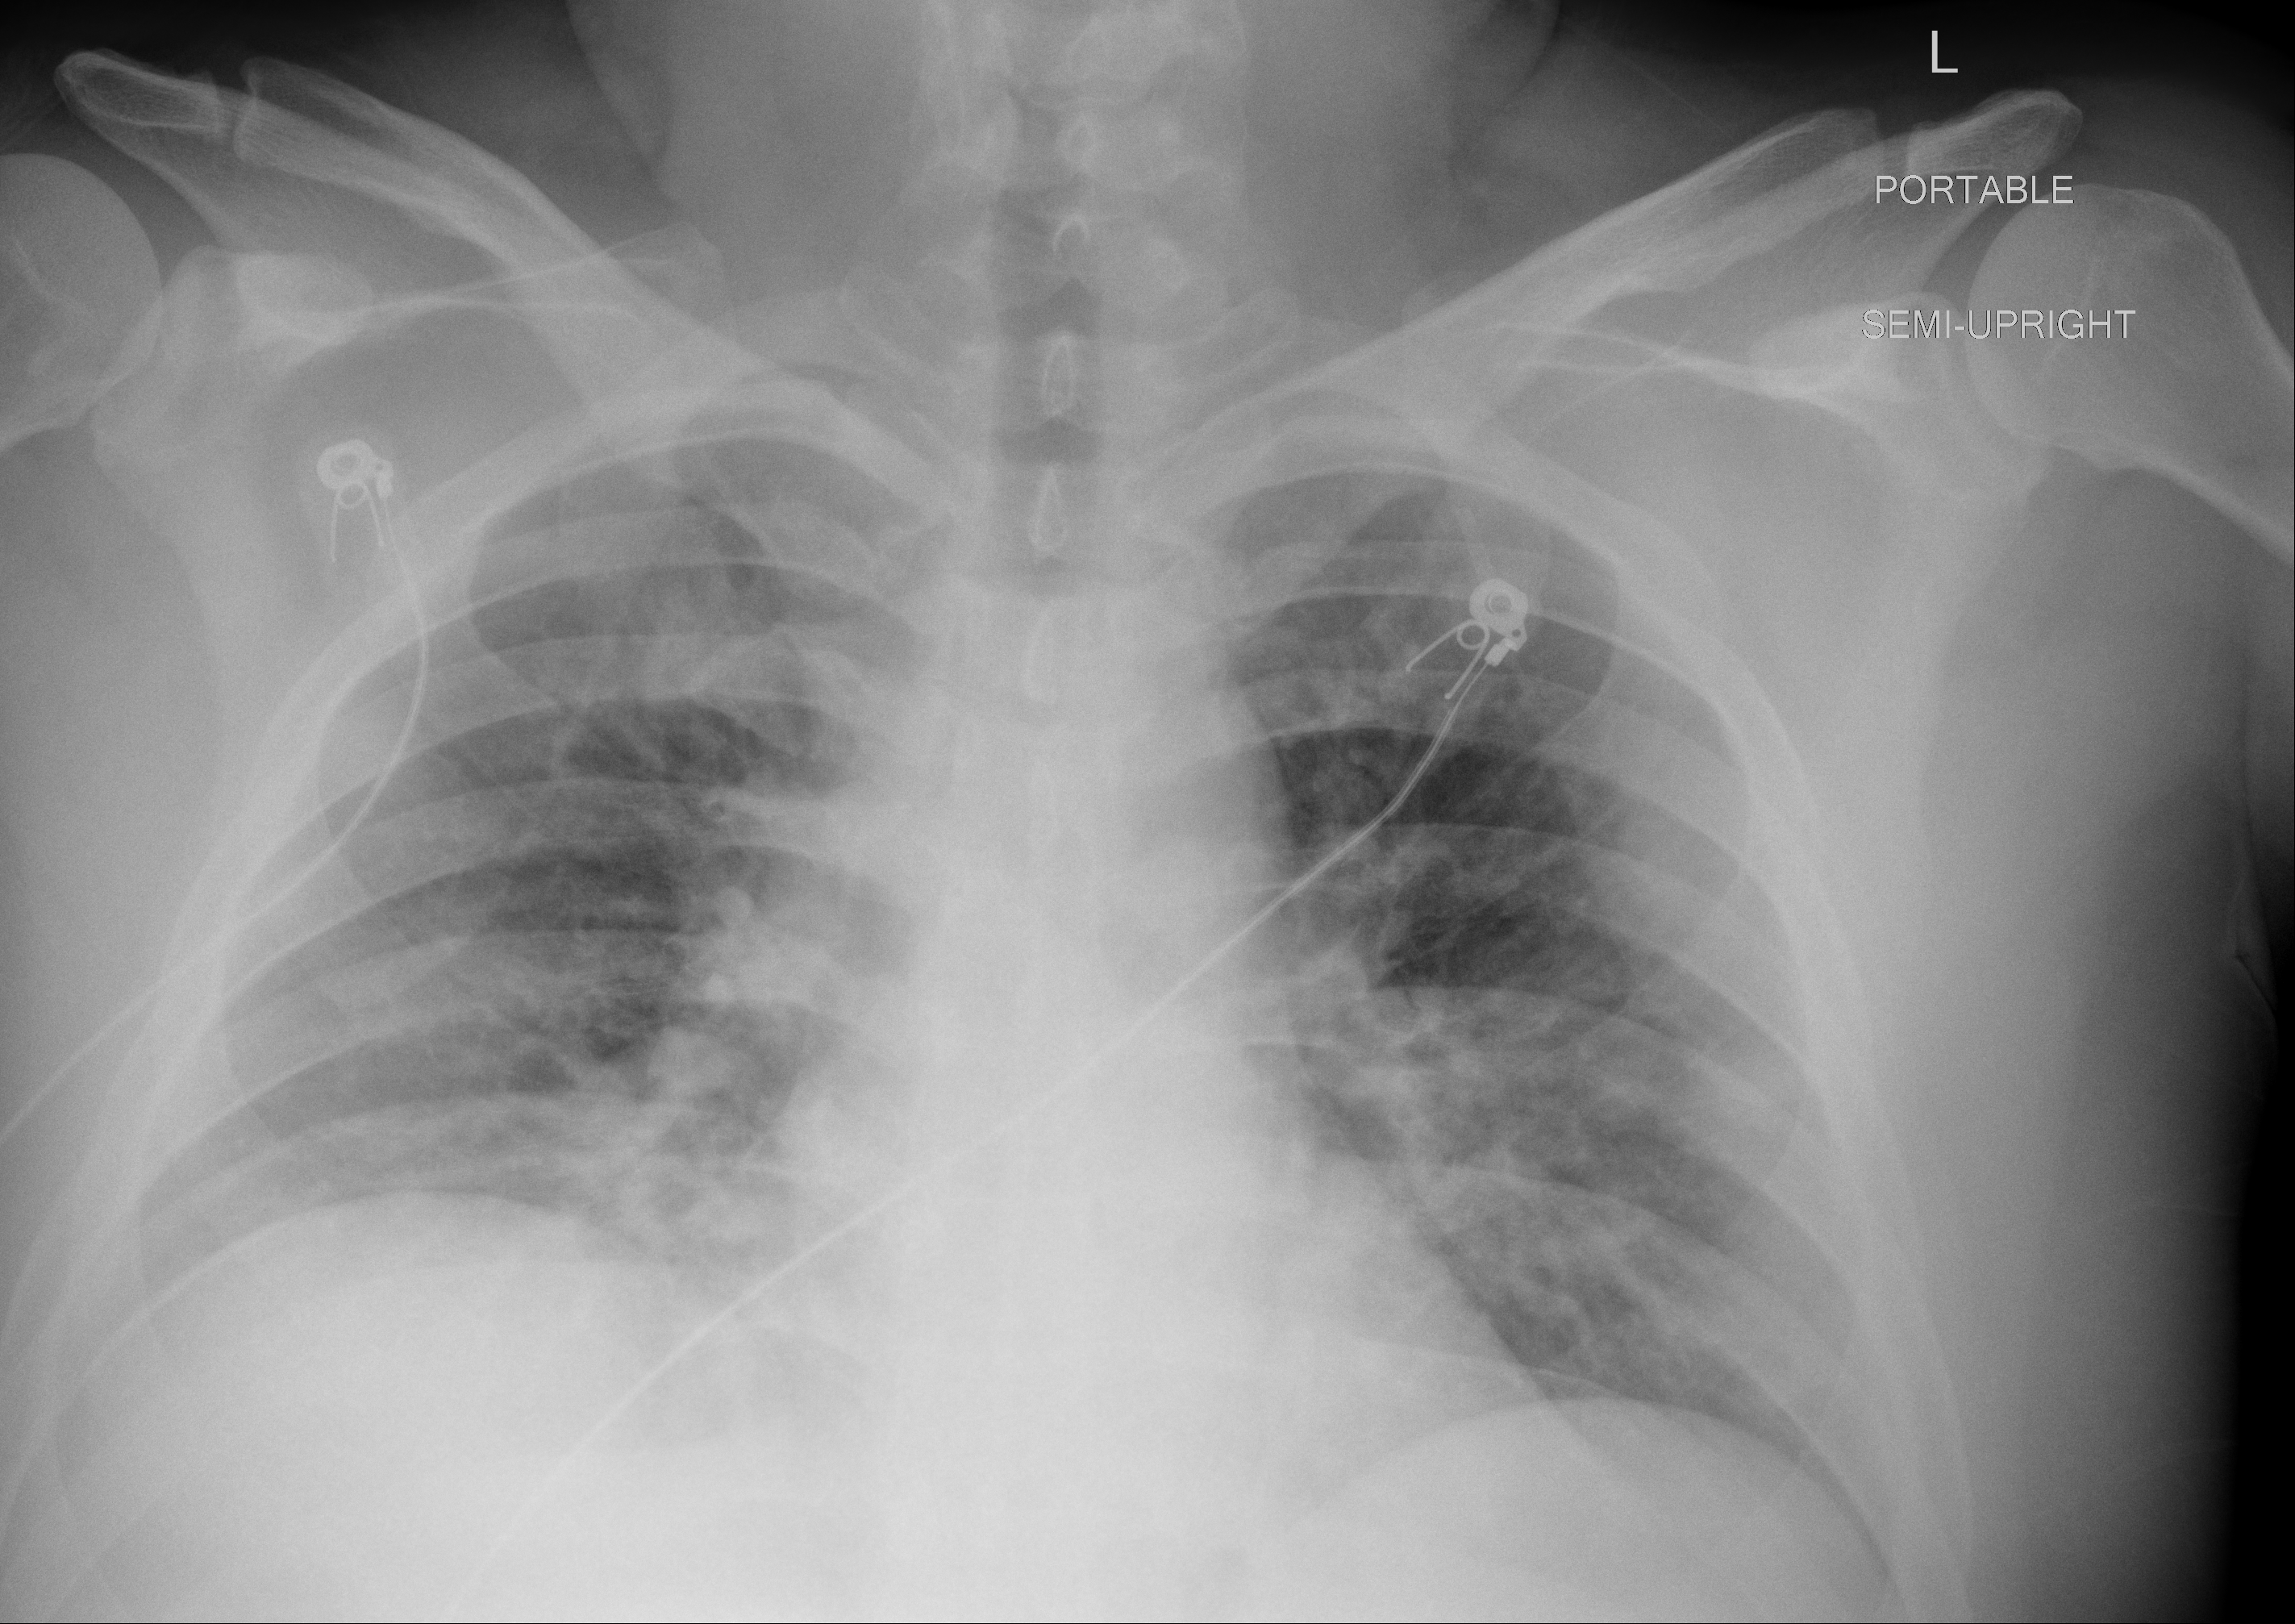
Chest radiograph, AP projection. Male patient, age 38 years; imaged 1 day after the COVID-19 diagnosis.
Key findings recorded by the radiologist: interval decrease in aeration of the lungs with stable to worsening bilateral lower lobe peribronchovascular airspace disease.